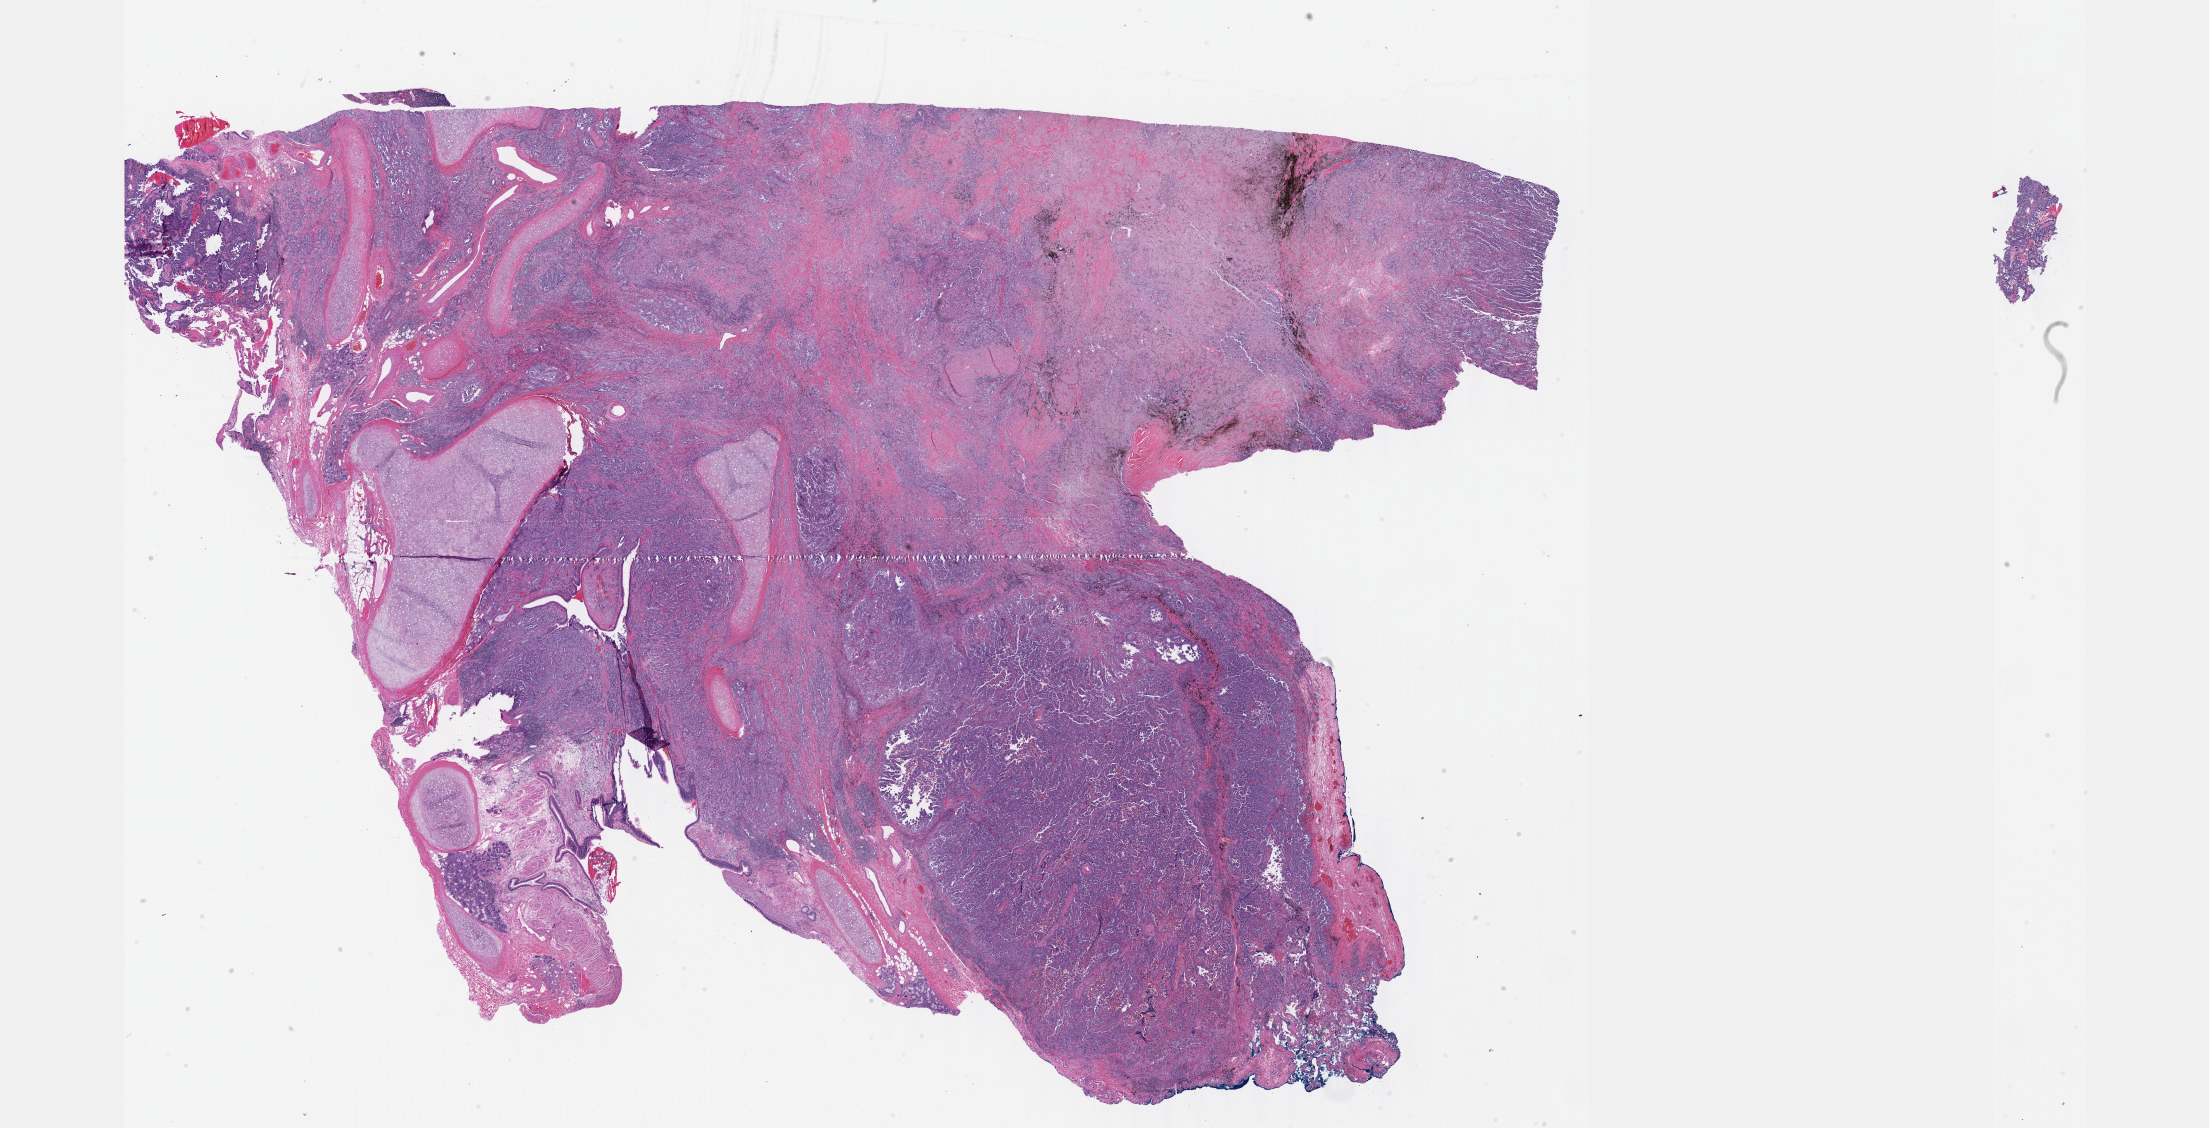
H&E-stained whole-slide image — shown as a low-resolution overview of the whole scanned area (about 35.7 x 18.2 mm). Formalin-fixed paraffin-embedded (FFPE) diagnostic section. Primary tumour sample from the lung. Male, age 69 years at initial diagnosis.
• pathologic diagnosis: Adenocarcinoma, NOS (lower lobe, lung)
• laterality: left
• AJCC pathologic stage: IIA (7th edition)